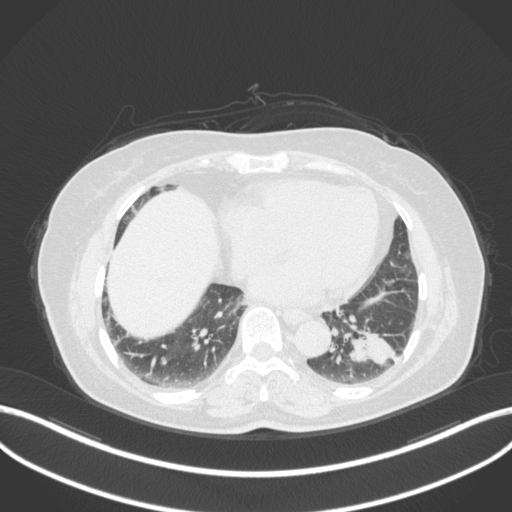
Chest CT, one axial slice; position 133 of 307 along the scan axis; reconstruction kernel B31f; 120 kVp; lung window (W 1500 / L -600 HU); 512 × 512 image matrix, field of view 400 × 400 mm. Patient: female, 59 years. Case-level facts recorded for this patient, not image findings: clinical TNM (as recorded): T2a N0 M0; histopathological grade: G2-3.
Annotated regions visible in this slice (bounding box drawn by a radiologist):
- lung tumour (recorded histology: adenocarcinoma): bounding box (x1, y1, x2, y2) in pixels: (344, 324, 401, 368)